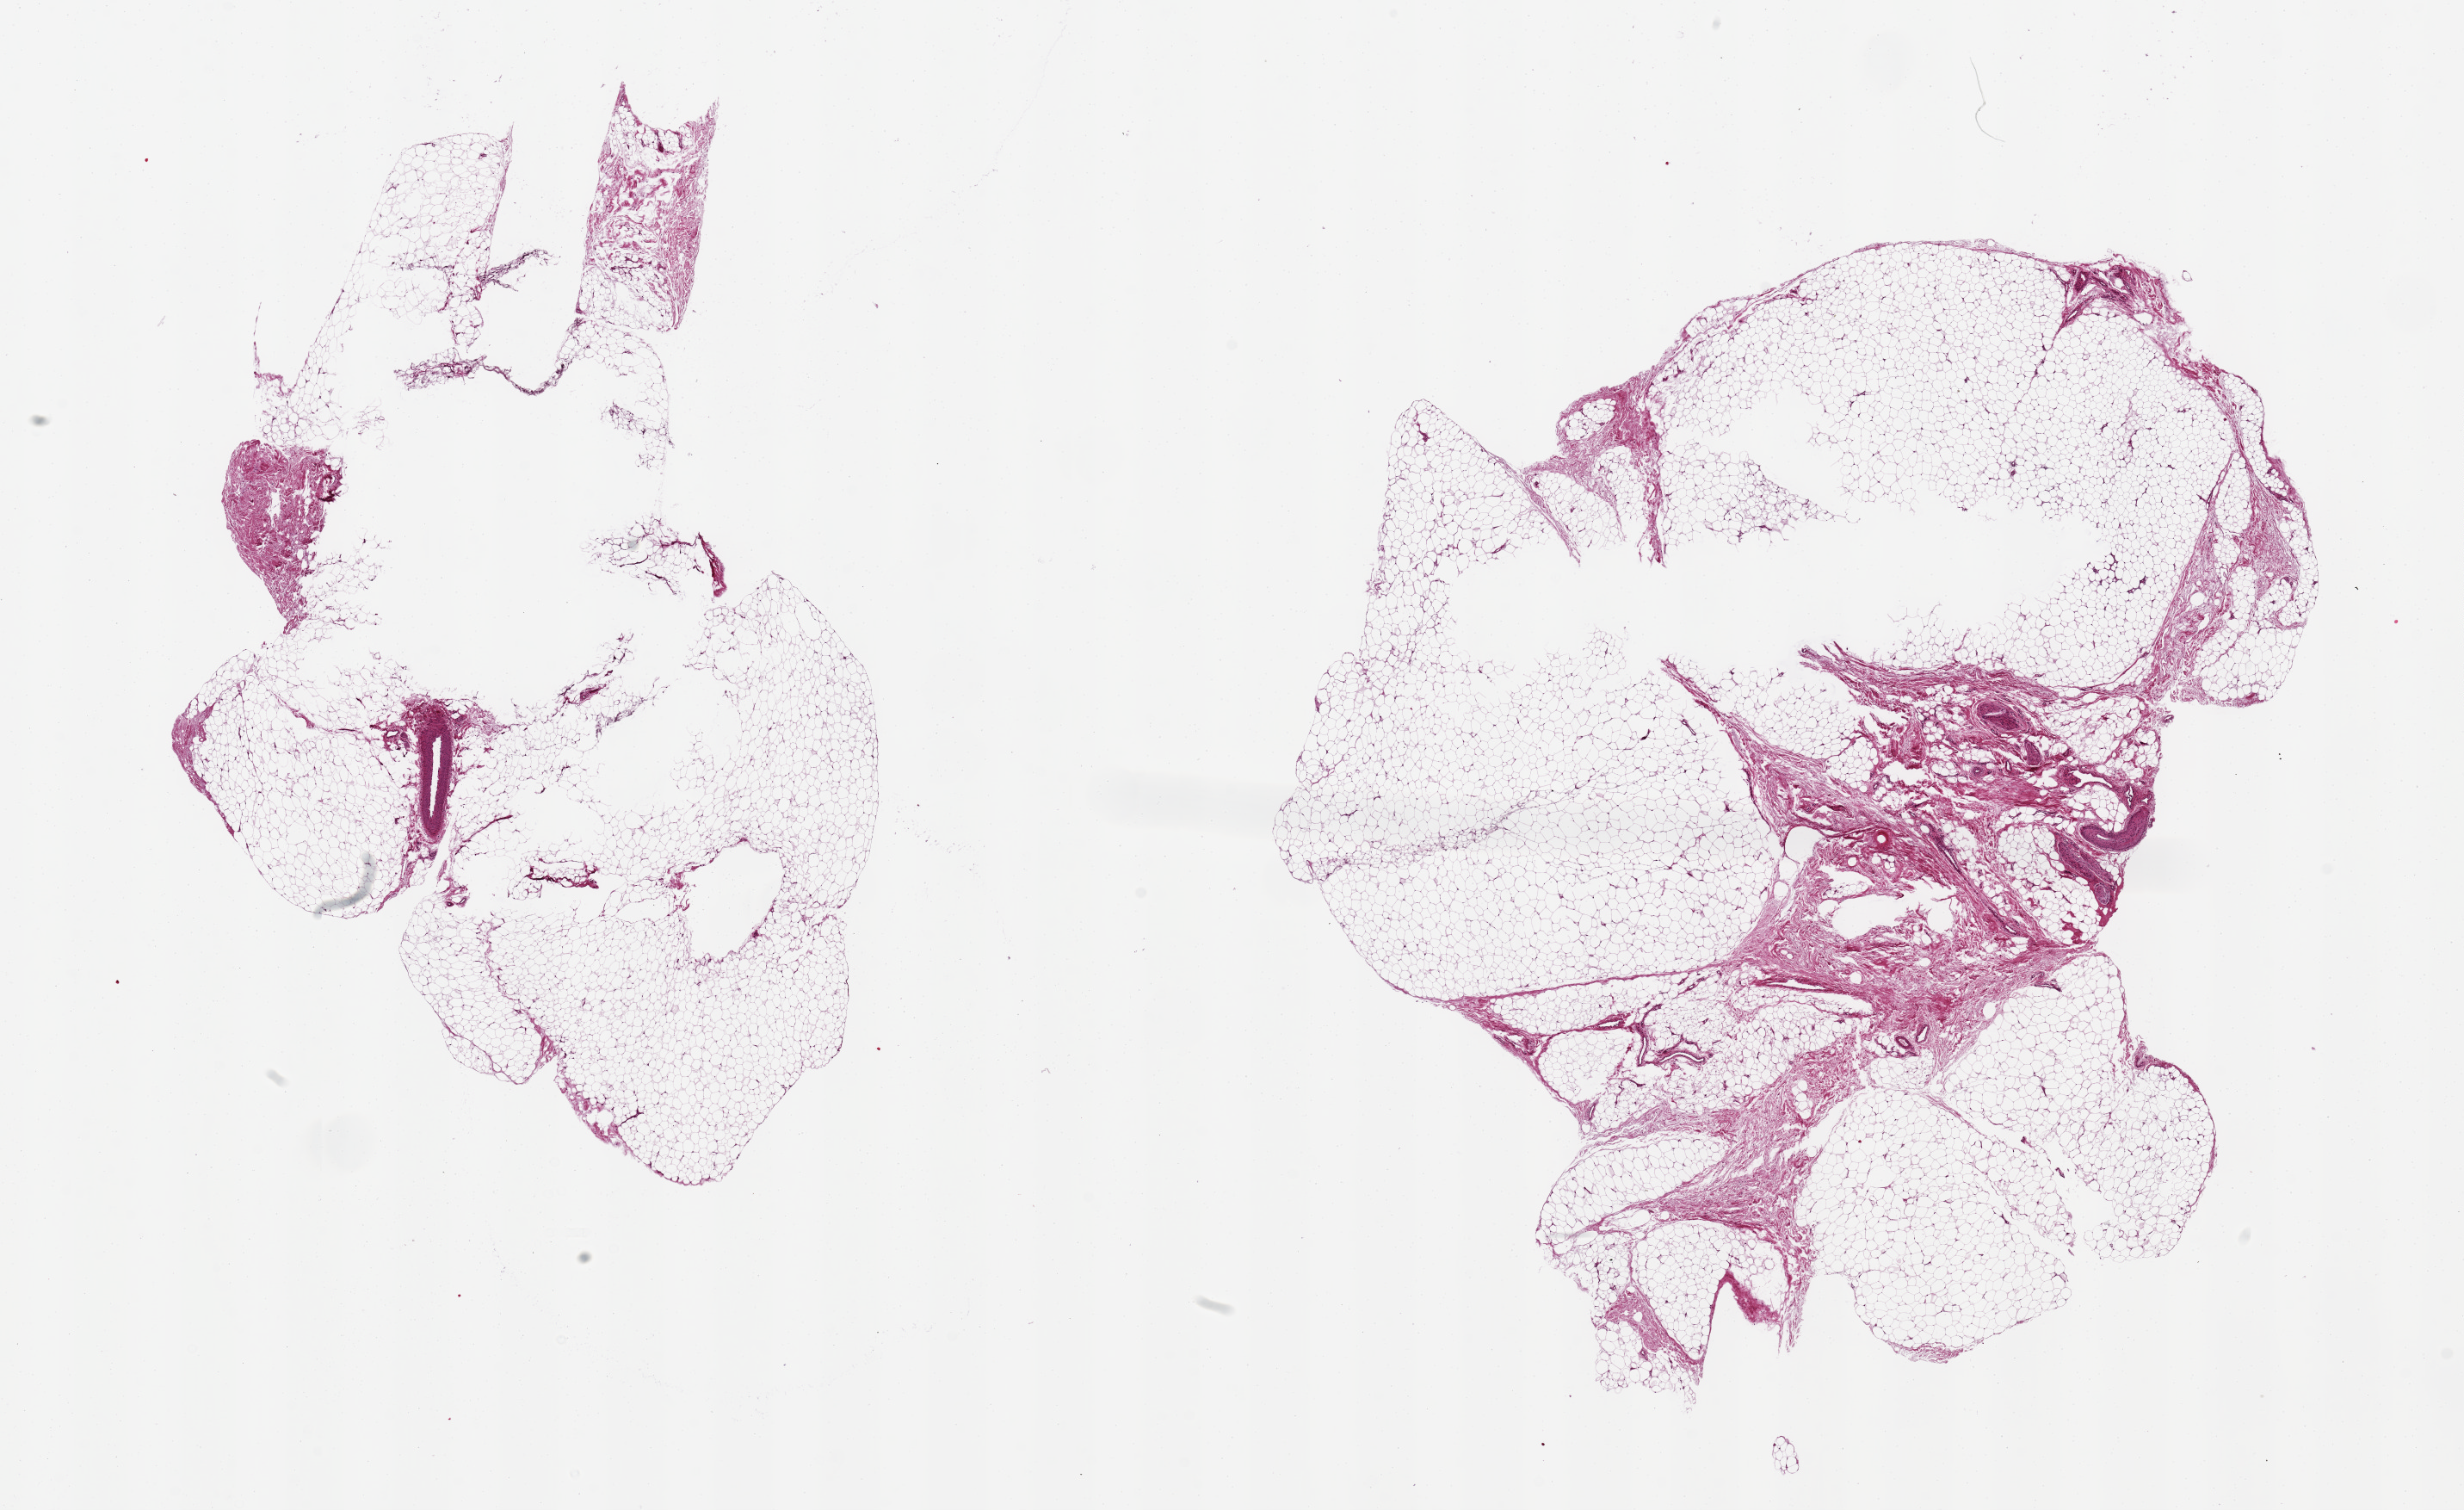
Whole-slide image, H&E stain, brightfield — a low-resolution overview of the entire scanned area, about 22.6 x 13.9 mm. PAXgene-fixed paraffin-embedded (PFPE) section. Sampled site (target tissue): adipose tissue. Tissue donor sample. Male donor.
* review note (as recorded): 2 aliquots